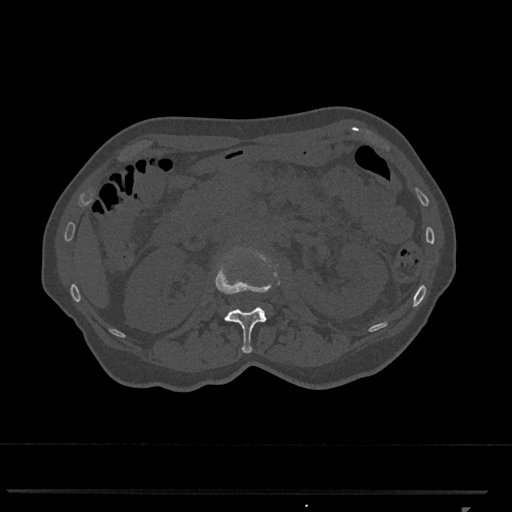
CT including the spine, one axial slice. Slice 385 of 793 in the series (ordered by position). 120 kVp. Bone window (W 1800 / L 400 HU). 512 × 512 image matrix, field of view 380 × 380 mm. Patient: female, 62 years. Case-level facts recorded for this patient, not image findings: primary cancer: renal.
Outlined on this slice (semi-automatic segmentation, software-assisted and operator-edited):
- L1 vertebra: bounding box (x1, y1, x2, y2) in pixels: (215, 249, 280, 353)